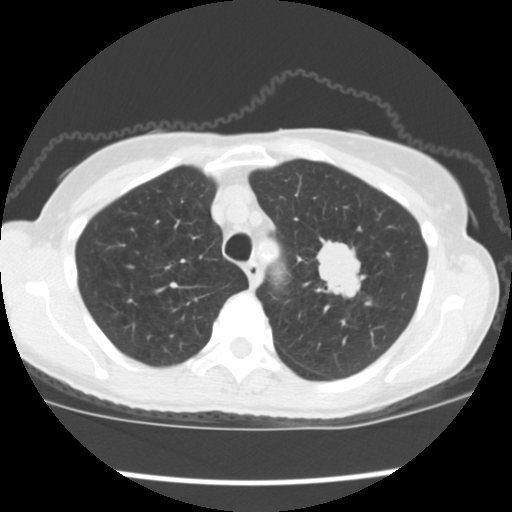
Low-dose screening chest CT, one axial slice; slice 142 of 176 in the series (ordered by position); reconstruction kernel STANDARD; 120 kVp; lung window (W 1500 / L -600 HU); 2.5 mm slice thickness; 512 × 512 image matrix, field of view 318 × 318 mm.
Structures marked on this image (outlined manually by an expert reader):
- lesion 1 (tumor, upper lobe of left lung): bounding box <317,238,365,298> (left, top, right, bottom; pixels)